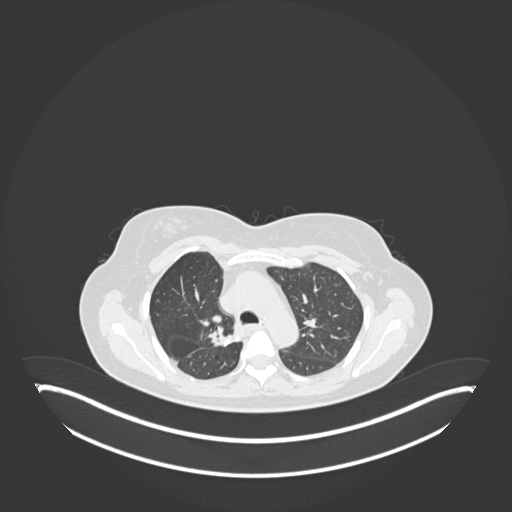
Chest CT, one axial slice. Position 121 of 181 along the scan axis. 120 kVp. Lung window (W 1500 / L -600 HU). 512 × 512 image matrix, field of view 500 × 500 mm. Female patient, age 65 years. Case-level facts recorded for this patient, not image findings: clinical TNM (as recorded): T1b N0 M0; histopathological grade: G2.
Annotated regions visible in this slice (rectangle marked by the reading radiologist):
- lung tumour (recorded histology: adenocarcinoma): bounding box (x1, y1, x2, y2) in pixels: (210, 328, 244, 351)